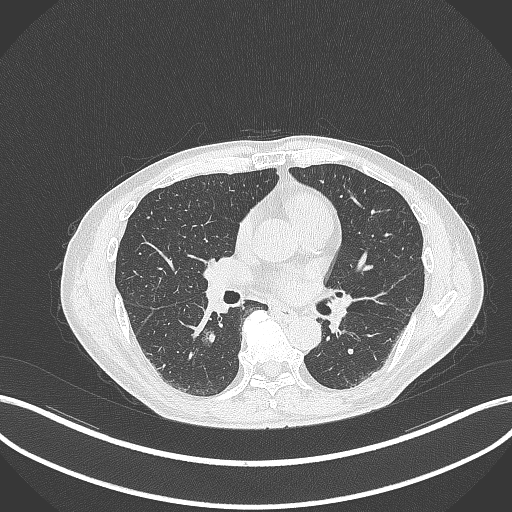
Chest CT, one axial slice. Position 162 of 323 along the scan axis. Reconstruction kernel B70f. 120 kVp. Lung window (W 1500 / L -600 HU). 1 mm slice thickness. 512 × 512 image matrix, field of view 400 × 400 mm. Male patient, age 61 years. From the clinical record (not read from this slice): clinical TNM (as recorded): T1c N0 M0.
Annotated regions visible in this slice (rectangle marked by the reading radiologist):
- lung tumour (recorded histology: adenocarcinoma): bounding box (x1, y1, x2, y2) in pixels: (200, 326, 219, 348)